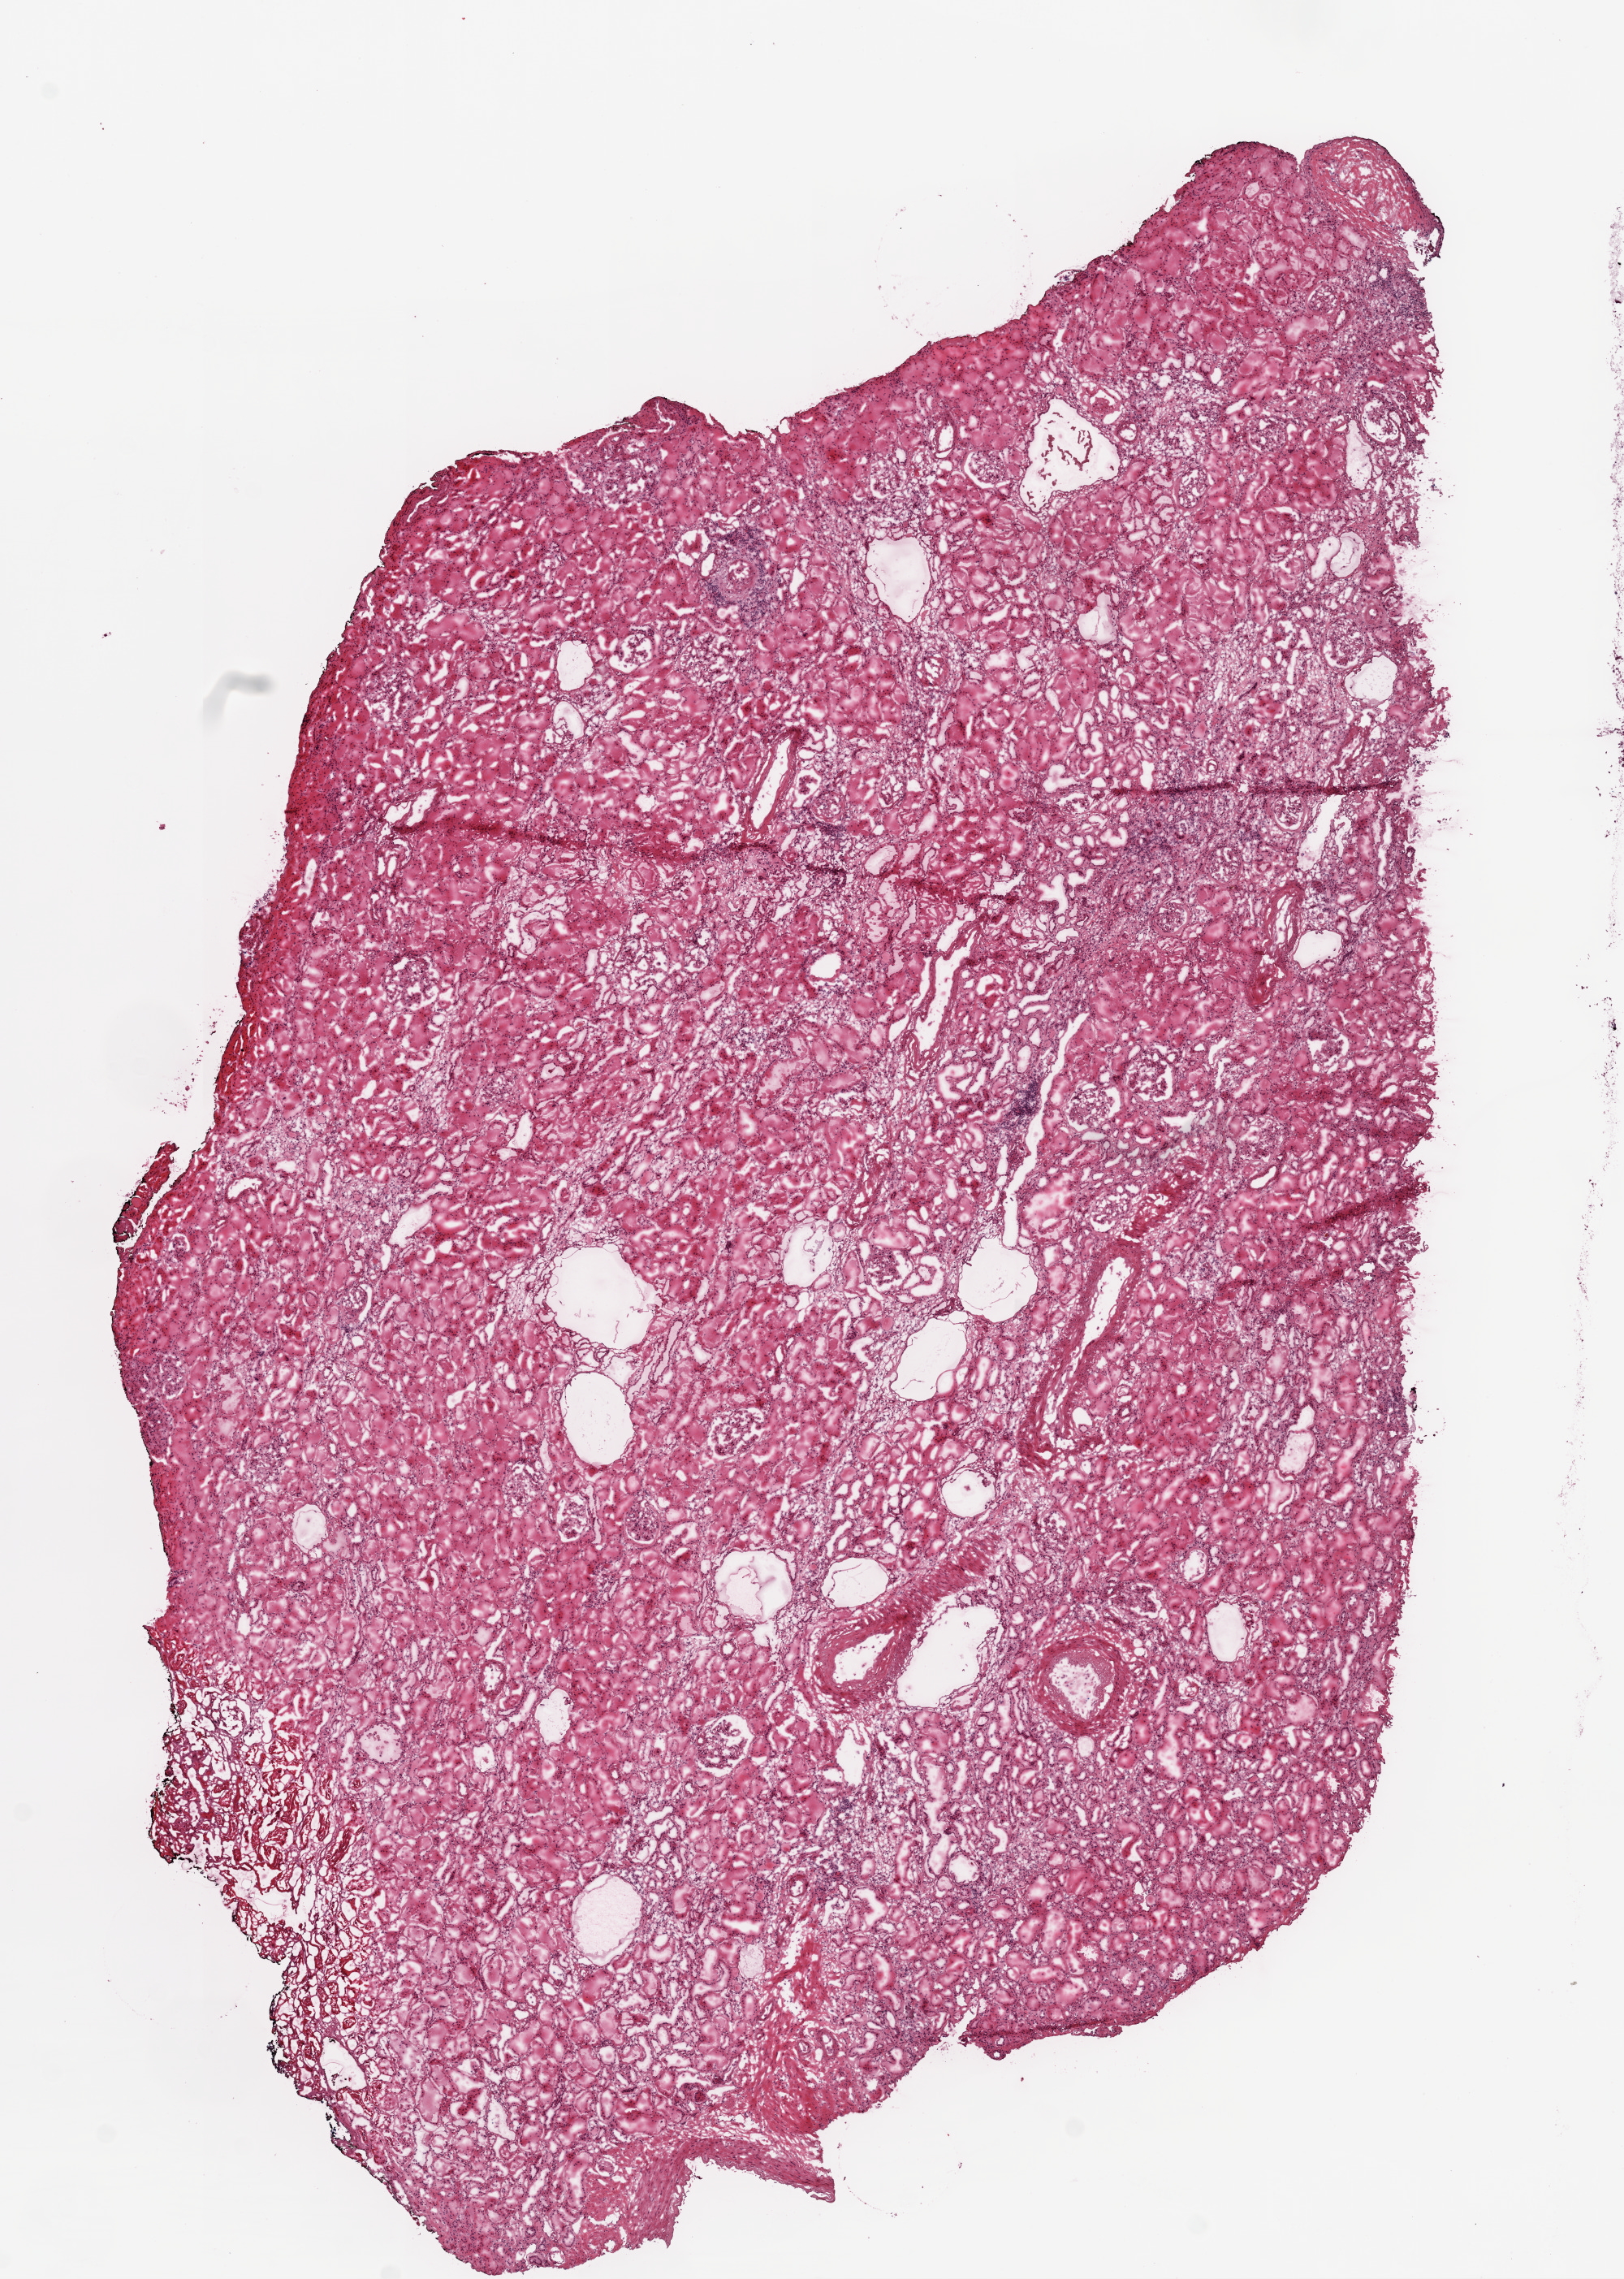
Whole-slide histology image, H&E, a low-resolution overview of the entire scanned area, about 8.0 x 11.3 mm (from a 20x scan); frozen section; kidney, solid tissue normal (non-tumour tissue) sample. Male, age 75 years at initial diagnosis.
This section: solid tissue normal (non-tumour) sample from the same patient. Patient diagnosis: Clear cell adenocarcinoma, NOS.